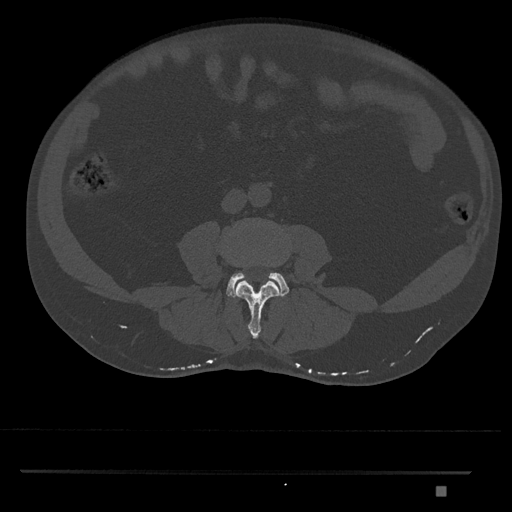
CT including the spine, one axial slice. Position 654 of 1134 along the scan axis. 120 kVp. Bone window (W 1800 / L 400 HU). 512 × 512 image matrix, field of view 429 × 429 mm. Male patient, age 65 years. Case-level facts recorded for this patient, not image findings: primary cancer: prostate.
Annotated regions visible in this slice (semi-automatic segmentation, software-assisted and operator-edited):
- L3 vertebra: bounding box [x1, y1, x2, y2] px = [235, 281, 281, 339]
- L4 vertebra: [226, 272, 289, 298]